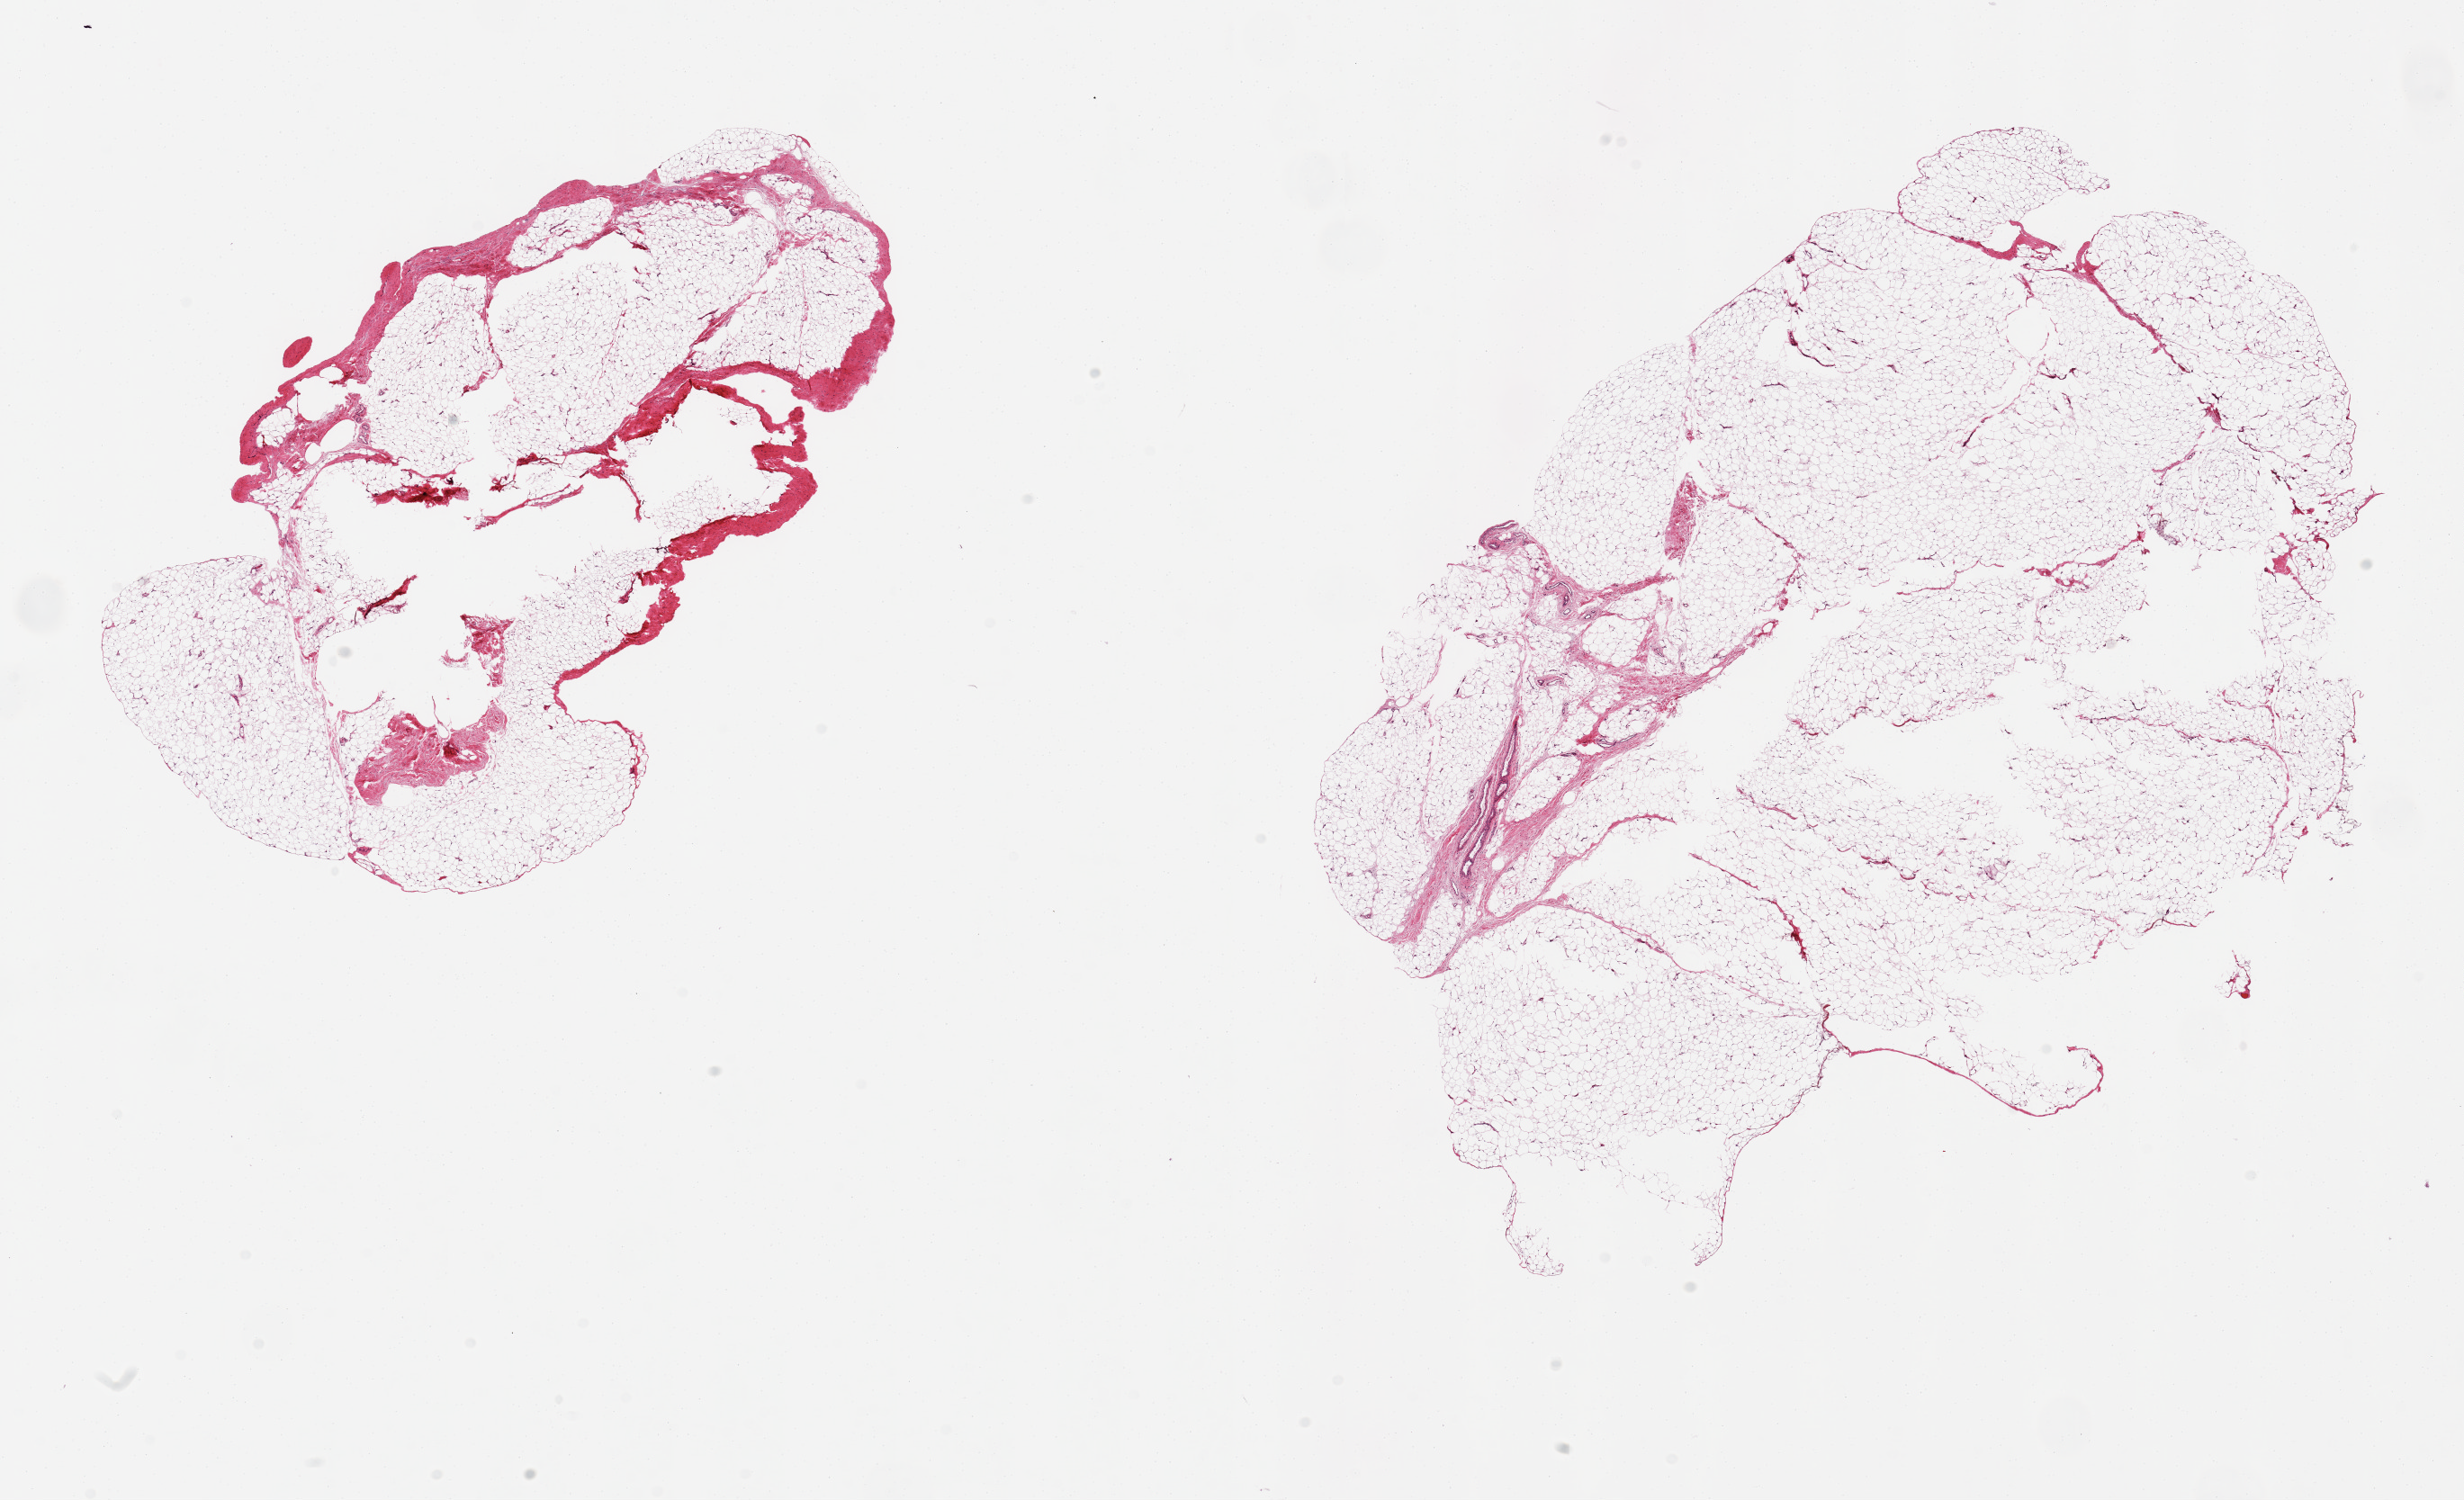
Whole-slide image, hematoxylin and eosin (H&E) stain — shown as a low-resolution overview of the whole scanned area (about 21.7 x 13.2 mm, acquisition: 20x scan). PAXgene-fixed, paraffin-embedded tissue. Section of adipose tissue (target tissue). Tissue donor sample. Donor: male.
Reviewer comment on this tissue sample: 2 pieces, ~20$ fascia.